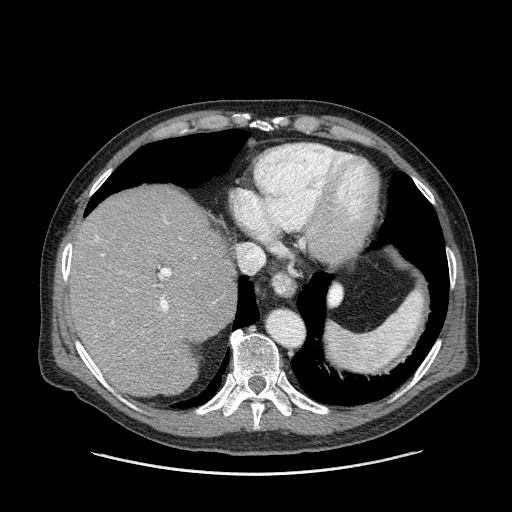
Contrast-enhanced abdominal CT (liver protocol), one axial slice. Position 118 of 180 along the scan axis. 120 kVp. One of 2 acquisitions stored at this slice position. Soft-tissue window (W 400 / L 40 HU). 512 × 512 image matrix. From the clinical record (not read from this slice): diagnosis: hepatocellular carcinoma (patient treated with transarterial chemoembolisation; whether this scan precedes or follows treatment is not stated here); TNM stage (as recorded): Stage-II; Child-Pugh class: A; tumour differentiation: well differentiated; tumour nodularity: multinodular.
Outlined on this slice (semi-automatic segmentation, software-assisted and operator-edited):
- liver parenchyma outside the tumour (the mass and vessels are separate outlines, so this box may not span the whole liver): bounding box (x1, y1, x2, y2) in pixels: (70, 188, 236, 396)
- liver vessels: (95, 235, 172, 337)